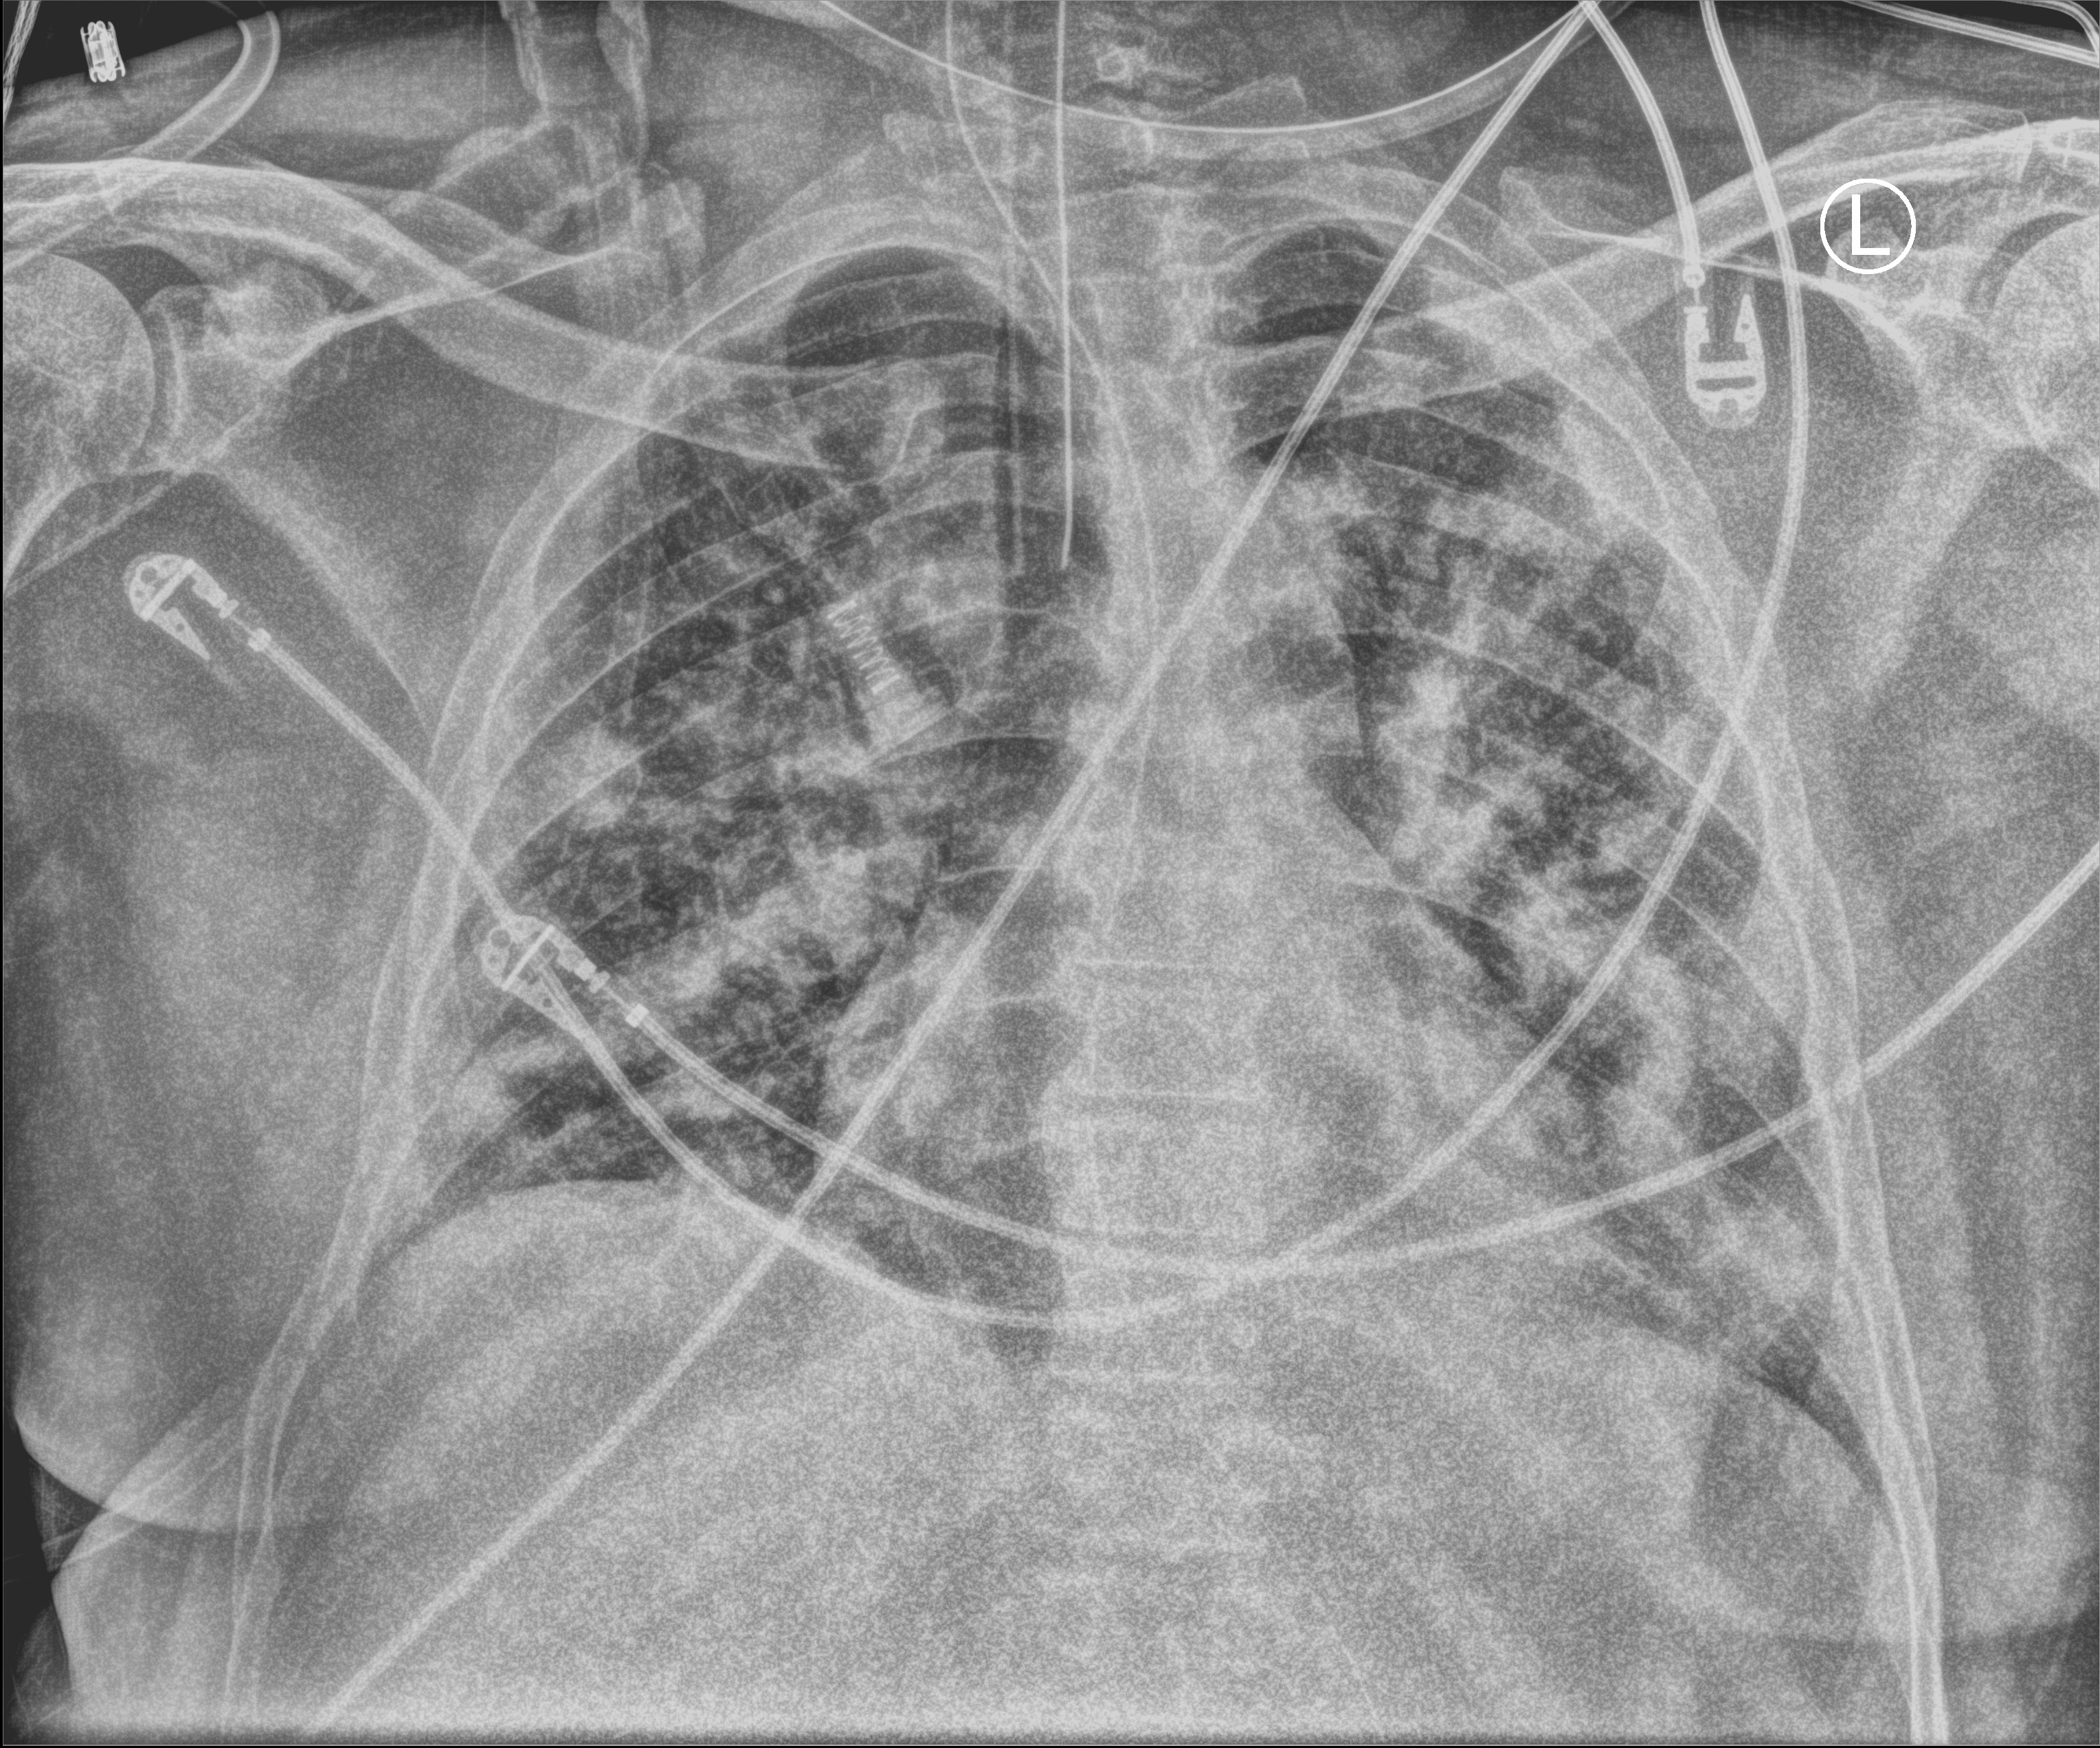
Bedside chest radiograph (computed radiography). Patient hospitalised with COVID-19; male, aged 18–59 years.
Hospital-stay facts (about this admission, not read from this image; timing relative to this image not recorded): other chronic lung disease (admission record): yes; length of hospital stay: 15 days; mechanically ventilated during this hospital stay: yes.